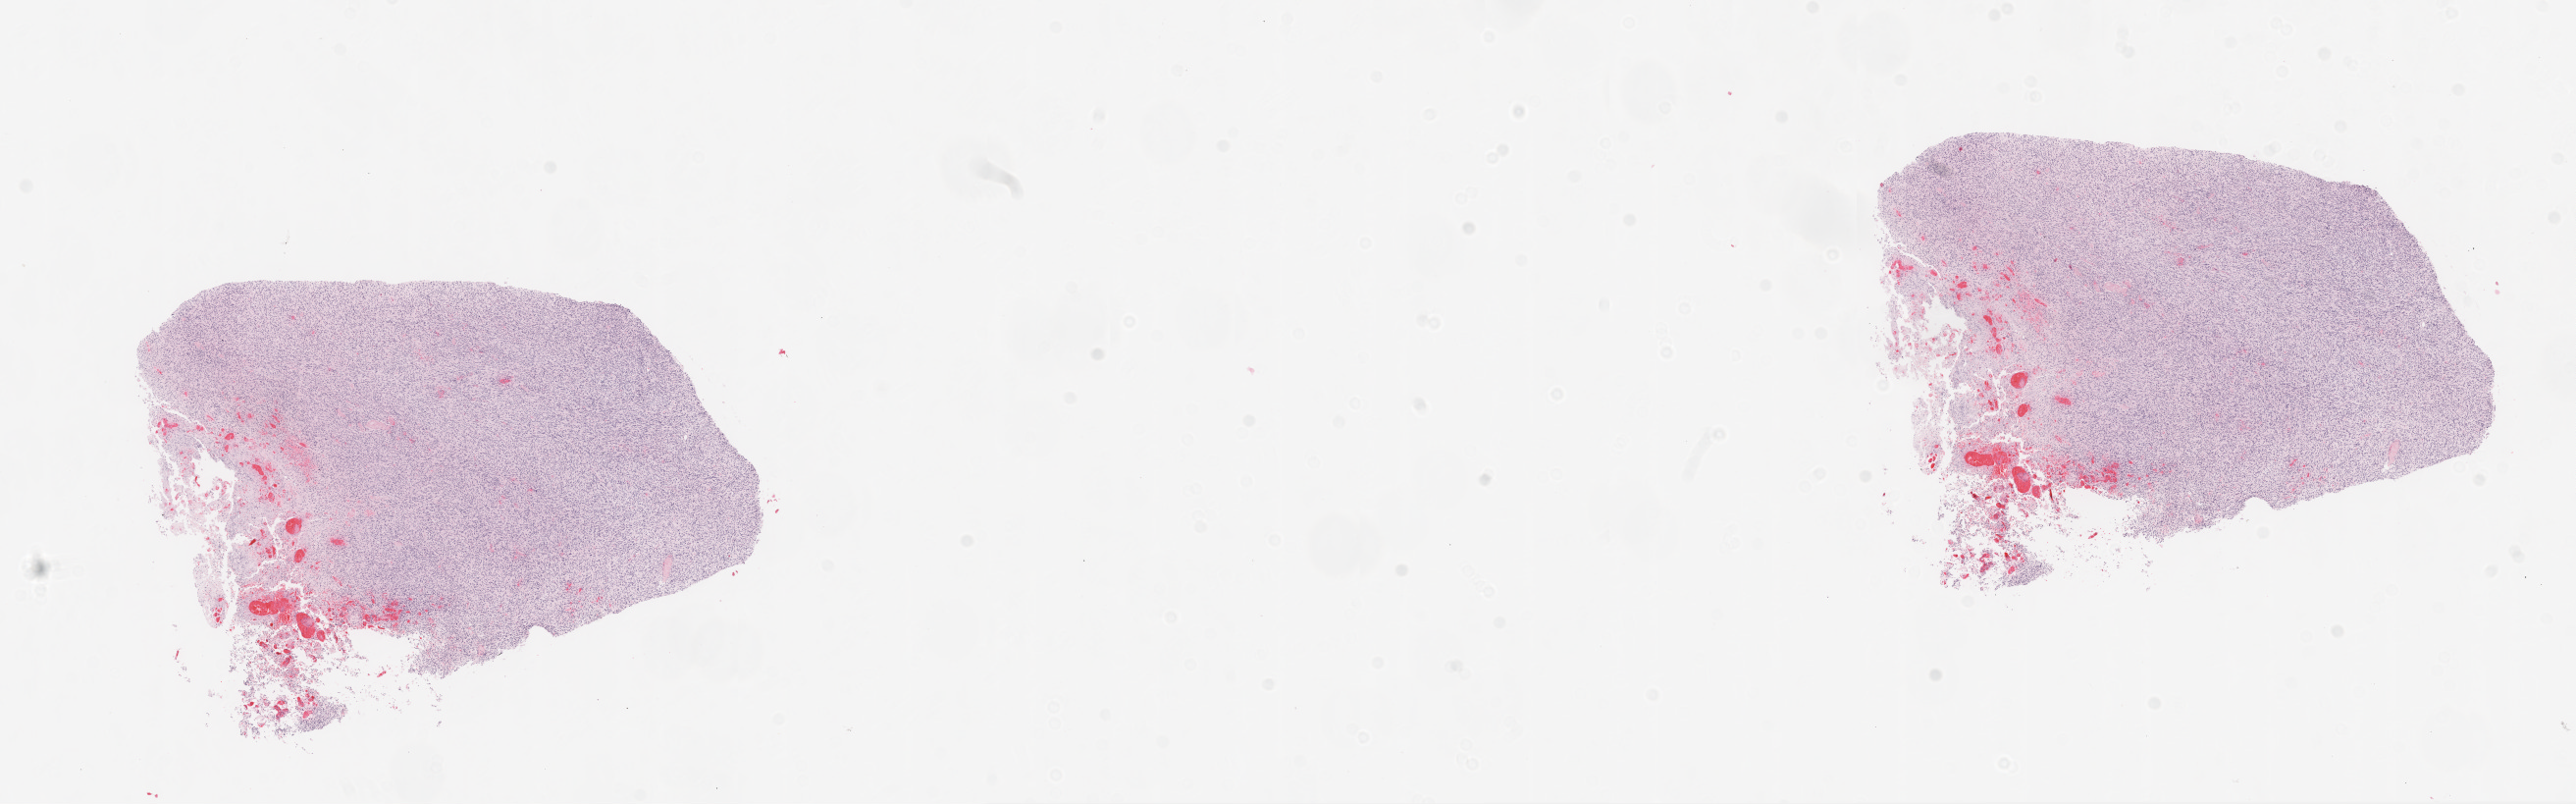
Digitized Hematoxylin and eosin (H&E) stained tissue section (whole slide), whole scanned area (about 21.1 x 6.6 mm) shown as a low-resolution overview. Frozen section from the top of the tissue portion. Primary tumour sample from the brain. Female, age 74 years at initial diagnosis. Slide review estimates, as recorded: tumour cells 90%, tumour nuclei 85%, normal cells 0%, stromal cells 0%, necrosis 10%.
Diagnosis: Glioblastoma.